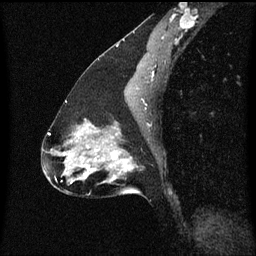
Breast MRI (dynamic contrast-enhanced), one sagittal slice; position 36 of 60 along the scan axis; dynamic contrast-enhanced series, image 2 of 3 at this slice position (ordered by acquisition); 1.5 T; TE 4.2 ms, TR 8.4 ms; 2 mm slice thickness; 256 × 256 image matrix, field of view 200 × 200 mm. Female patient, age 47 years.
Structures marked on this image (semi-automatically segmented with operator editing):
- analysis volume of interest (the breast-tissue region the enhancement analysis was run in; not a lesion): bounding box (x1, y1, x2, y2) in pixels: (85, 136, 143, 195)
- tumour enhancement mask (voxels above the 70 % enhancement threshold inside the analysis volume of interest): (85, 138, 134, 173)